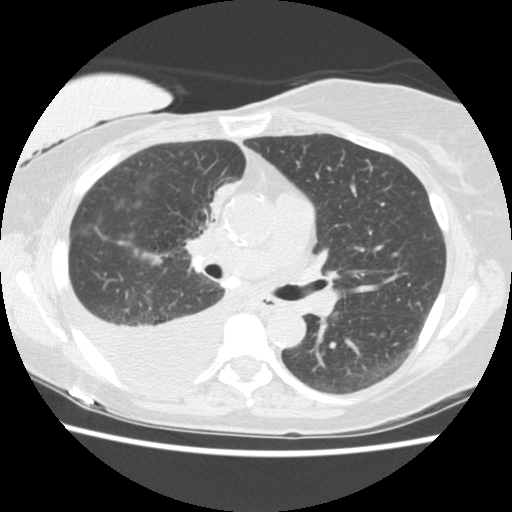
Low-dose screening chest CT, one axial slice. Slice 87 of 157 in the series (ordered by position). Reconstruction kernel STANDARD. Lung window (W 1500 / L -600 HU). 512 × 512 image matrix.
Annotated regions visible in this slice (manually delineated by an expert):
- lesion 1 (tumor, upper lobe of right lung): box from (x=210, y=181) to (x=239, y=217) px